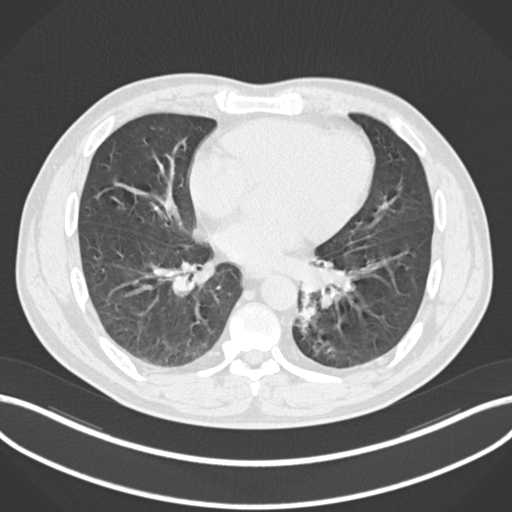
Chest CT, one axial slice; slice 90 of 223 in the series (ordered by position); reconstruction kernel B30f; lung window (W 1500 / L -600 HU); 1 mm slice thickness; 512 × 512 image matrix. Patient: male, 50 years. Case-level facts recorded for this patient, not image findings: clinical TNM (as recorded): T2a N3 M0.
Structures marked on this image (rectangle marked by the reading radiologist):
- lung tumour (recorded histology: squamous cell carcinoma): bounding box (x1, y1, x2, y2) in pixels: (294, 291, 318, 338)